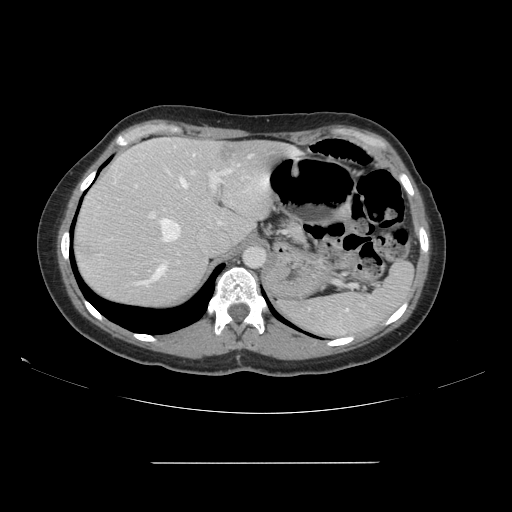
Contrast-enhanced abdominal CT, one axial slice. Slice 115 of 151 in the series (ordered by position). Intravenous contrast given. Soft-tissue window (W 400 / L 40 HU). 512 × 512 image matrix. Female patient, age 46 years. Case-level facts recorded for this patient, not image findings: diagnosis: colorectal cancer liver metastases, imaged before liver resection; multiple liver metastases: yes; largest metastasis: 3 cm; disease in both lobes: yes.
Annotated regions visible in this slice (expert manual segmentation):
- hepatic veins: bounding box (x1, y1, x2, y2) in pixels: (150, 154, 253, 242)
- liver: (74, 138, 295, 308)
- planned liver remnant (the part of the liver to remain after resection): (89, 138, 290, 252)
- portal vein (with intrahepatic branches): (134, 169, 234, 284)
- liver metastasis: (76, 241, 79, 248)
- liver metastasis: (219, 144, 240, 163)